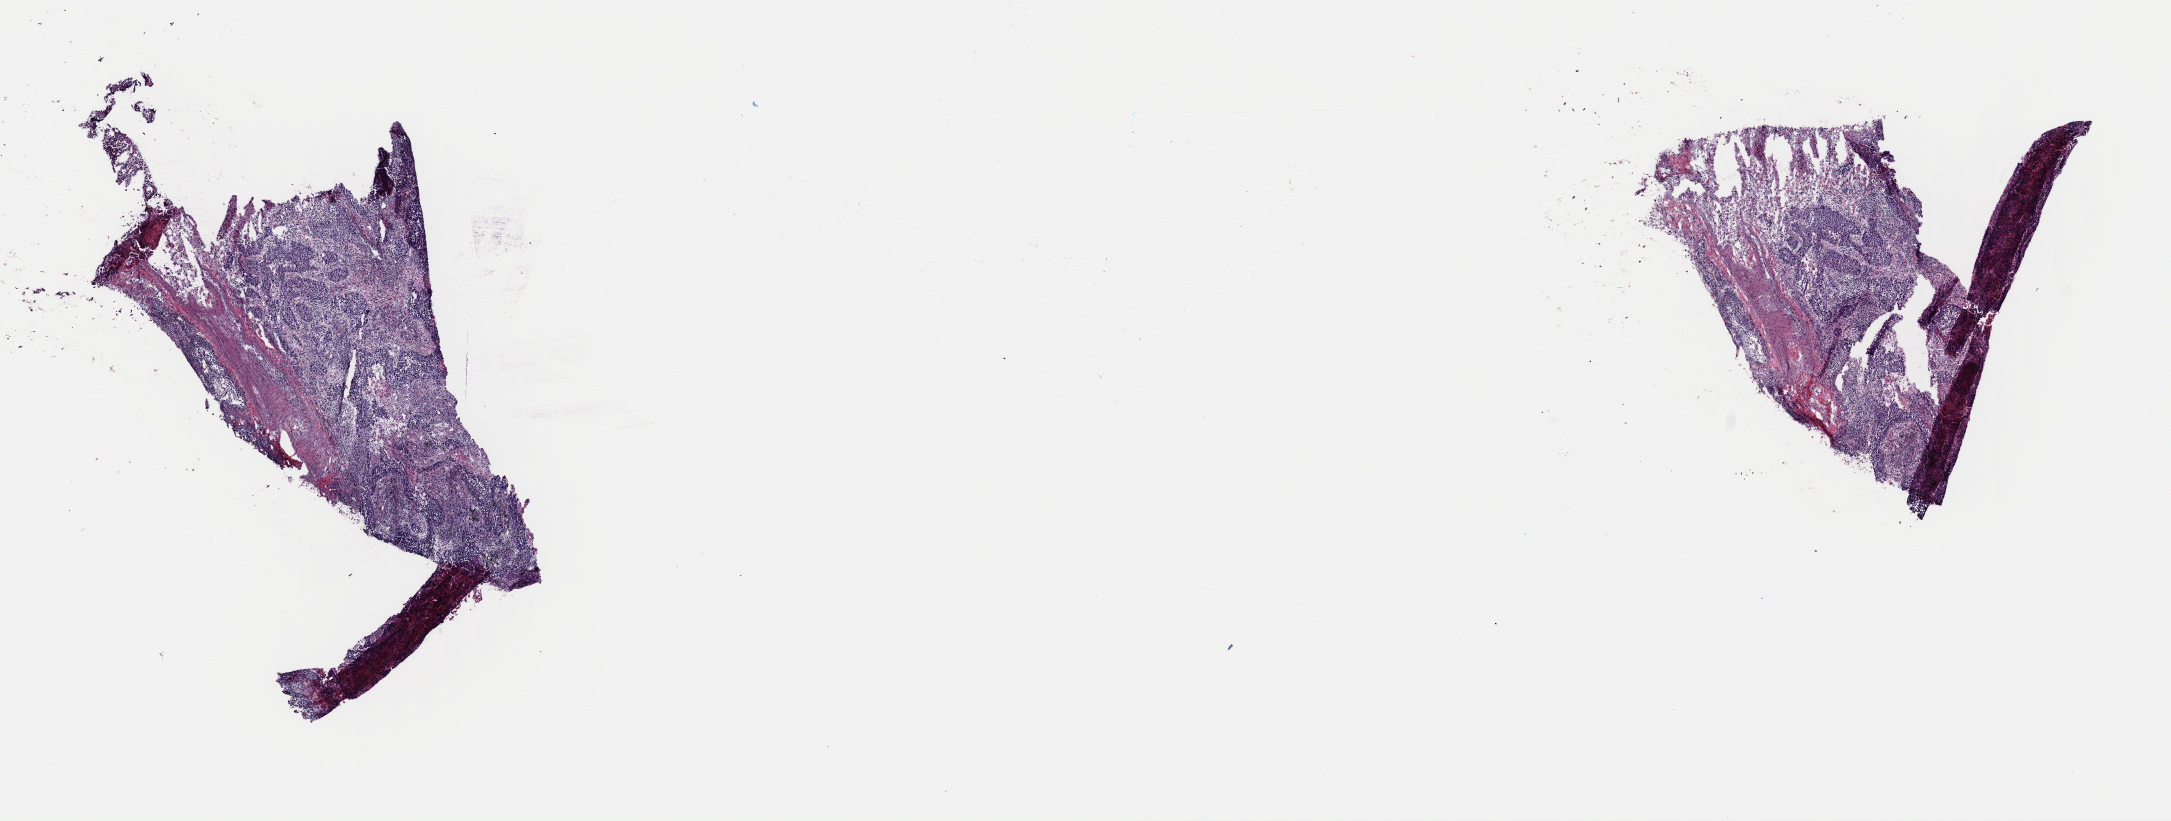
Hematoxylin and eosin (H&E) stained whole-slide image, whole scanned area (about 17.2 x 6.5 mm, acquisition: 40x scan) shown as a low-resolution overview, frozen section from the top of the tissue portion, sample: primary tumour, lung. Patient: male, age at initial diagnosis 63 years. Pathologist review of this section (percent, as recorded): tumour cells 50%, tumour nuclei 60%, normal cells 0%, stromal cells 40%, necrosis 10%. Inflammatory infiltration, as recorded: lymphocyte infiltration 50%, monocyte infiltration 50%, neutrophil infiltration 0%.
• AJCC pathologic stage: IA (6th edition)
• histologic diagnosis: Squamous cell carcinoma, NOS (upper lobe, lung)
• TNM: T1 N0 M0